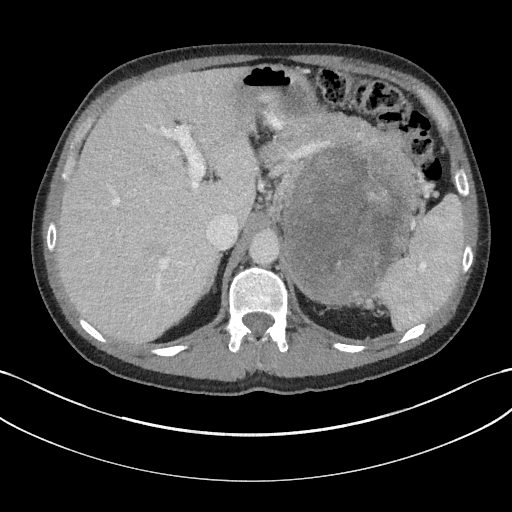
Contrast-enhanced abdominal CT, one axial slice; position 121 of 147 along the scan axis; reconstruction kernel I31f/3; intravenous contrast given; soft-tissue window (W 400 / L 40 HU); 3 mm slice thickness; 512 × 512 image matrix, field of view 384 × 384 mm. Patient: male, 58 years. Case-level facts recorded for this patient, not image findings: diagnosis: adrenocortical carcinoma; tumour side: left adrenal; tumour size at pathology: 22 cm; Ki-67 index: 26 %; stage (as recorded): 2.
Structures marked on this image (semi-automatic segmentation, software-assisted and operator-edited):
- mass: bounding box <284,151,410,300> (left, top, right, bottom; pixels)